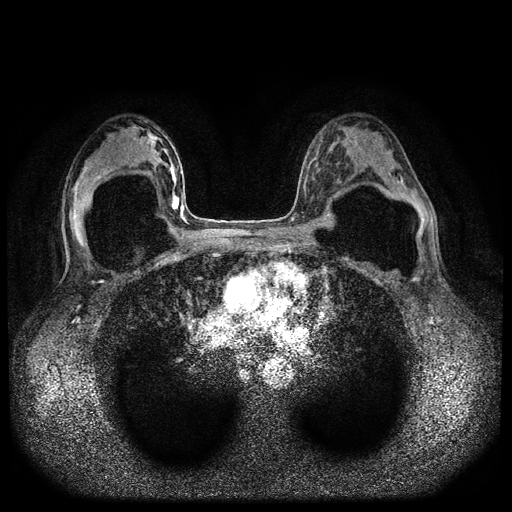
Breast MRI (dynamic contrast-enhanced, multi-phase), one axial slice; position 55 of 116 along the scan axis; dynamic contrast-enhanced series, time point 2 of 5 at this slice position (early post-contrast); 1.5 T; TE 2.6 ms, TR 5.4 ms; 2 mm slice thickness; 512 × 512 image matrix. Patient: female, 42 years.
Structures marked on this image (semi-automatically segmented with operator editing):
- breast lesion (labelled 'tumour' in the annotation; benign lesions carry a separate 'benign' label): box from (x=171, y=193) to (x=180, y=211) px